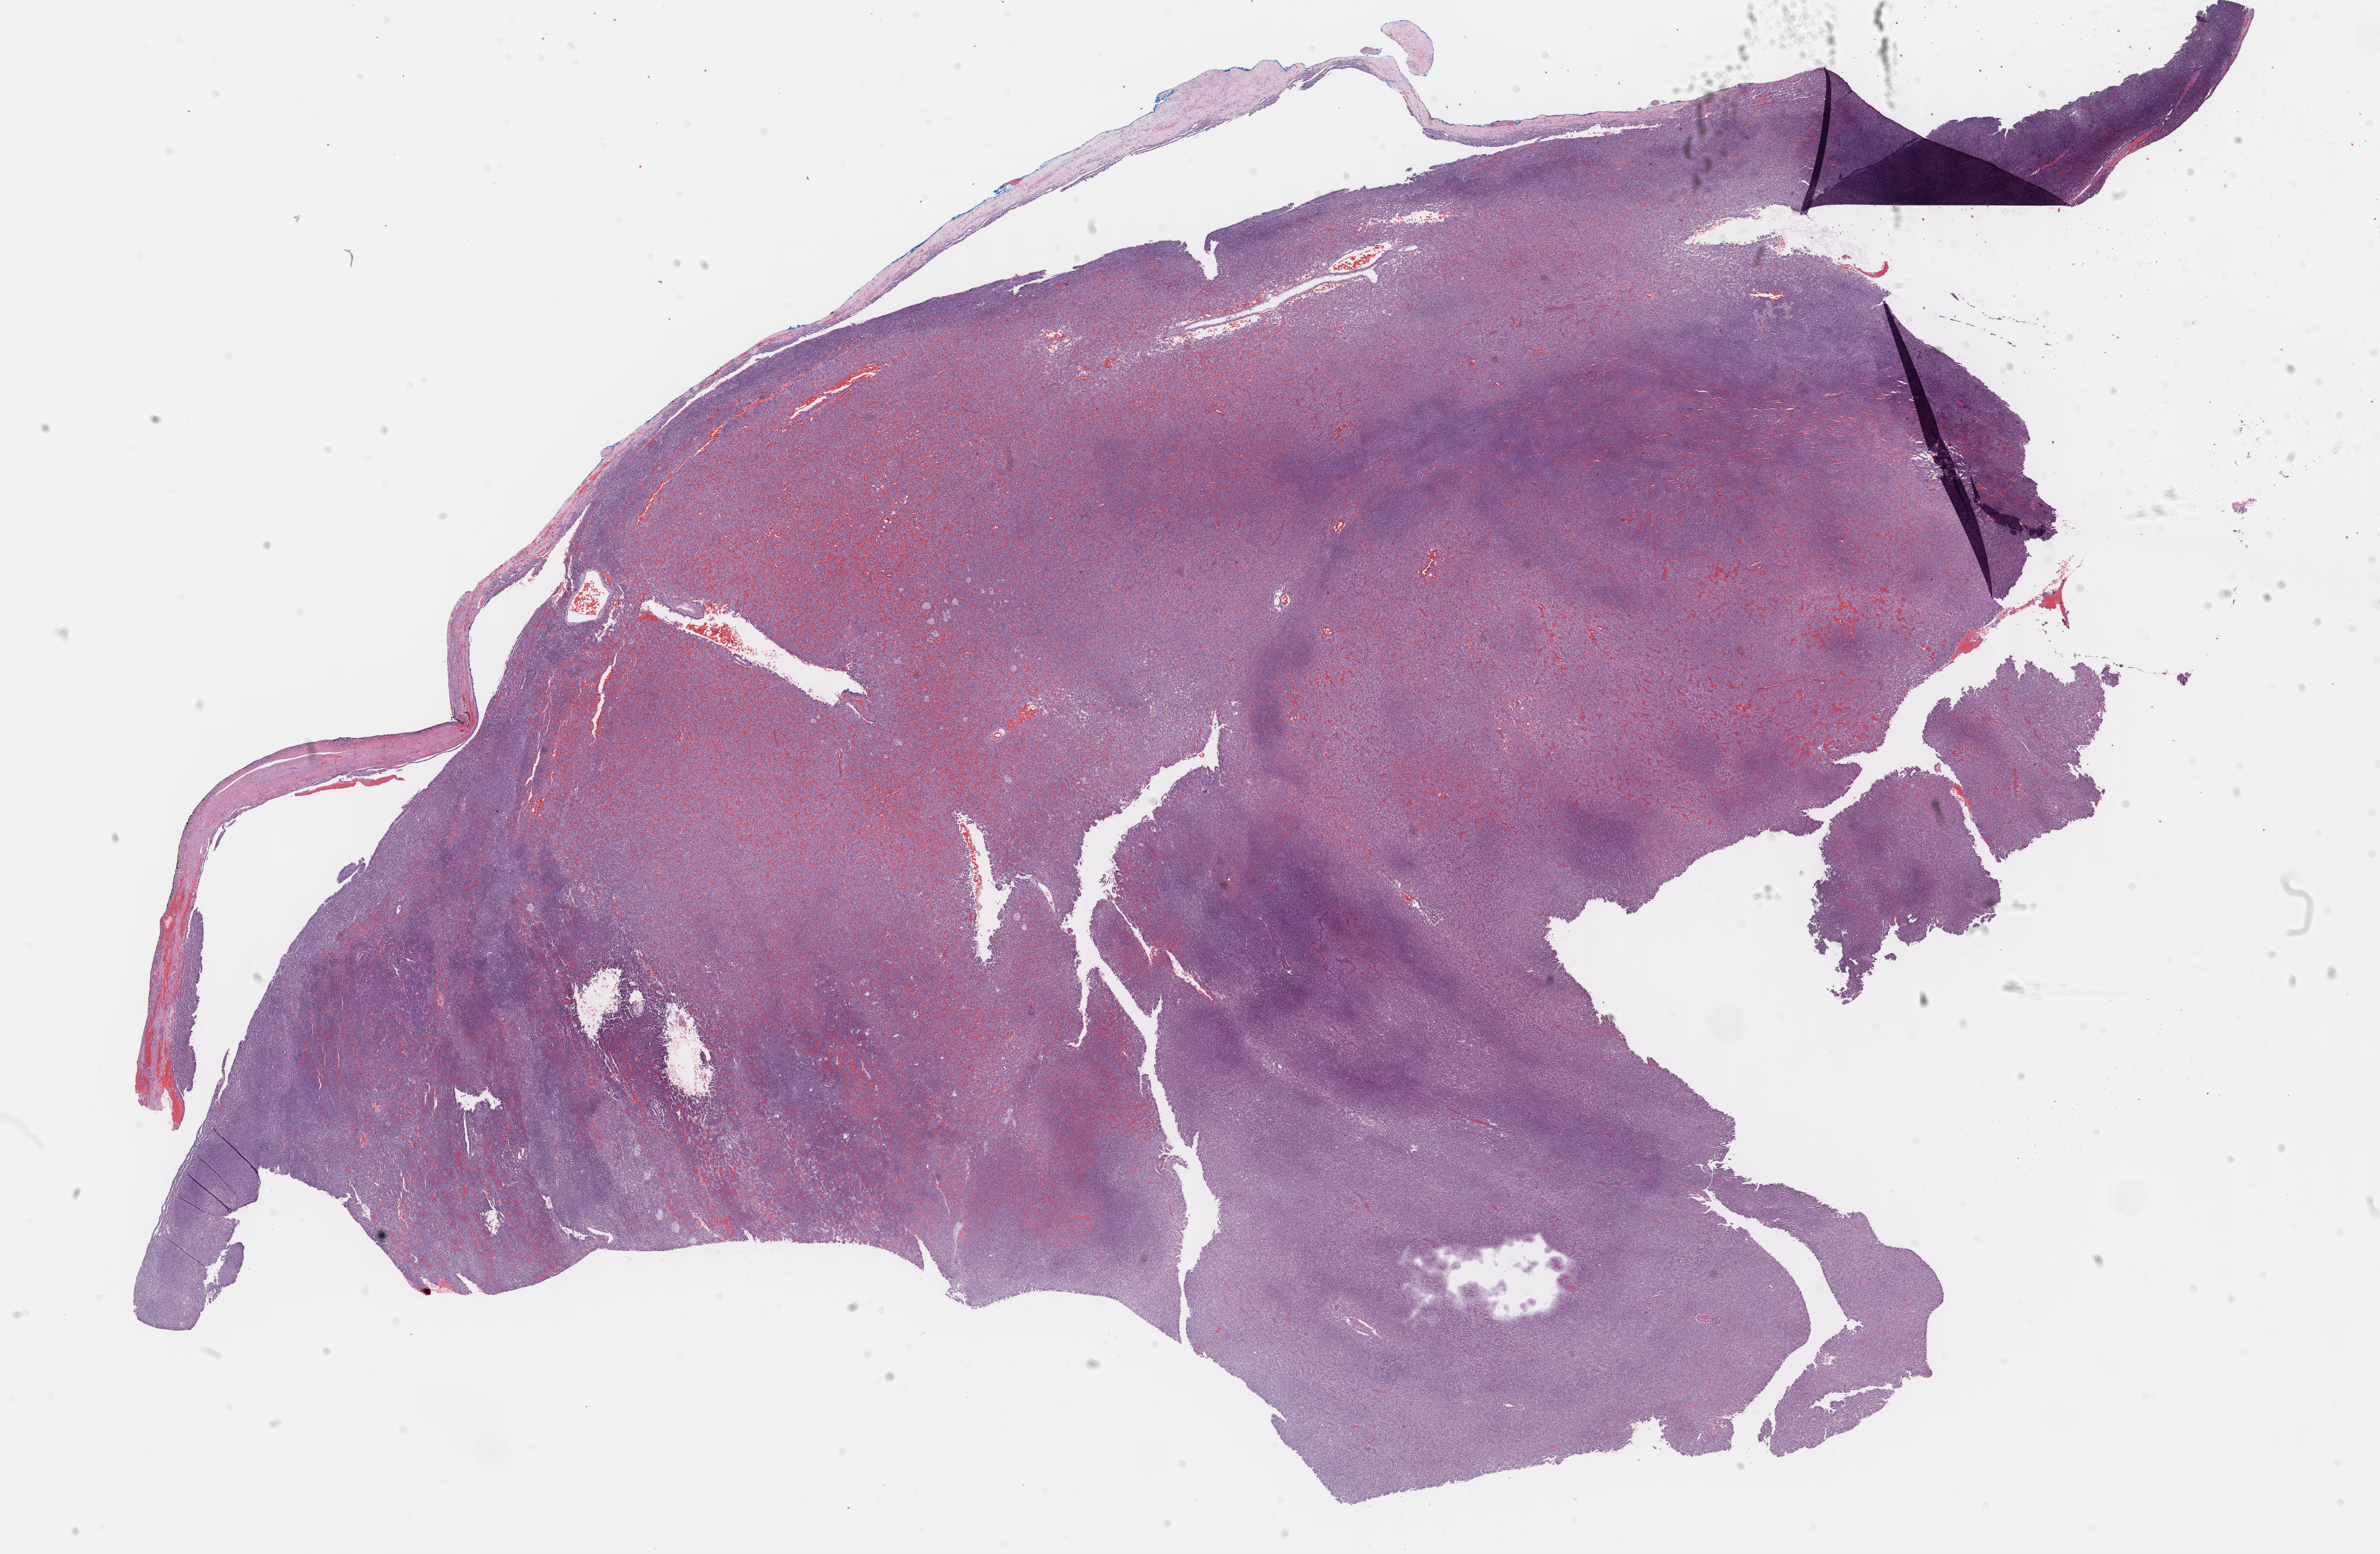
Whole-slide histology image, H&E, low-resolution overview of the scanned area, about 31.2 x 20.4 mm (acquisition: 40x scan); formalin-fixed paraffin-embedded (FFPE) diagnostic section; primary tumour sample from the kidney. Patient: male, age at initial diagnosis 62 years.
Pathologic diagnosis: Papillary adenocarcinoma, NOS. AJCC pathologic stage: I (6th edition). Laterality: left.